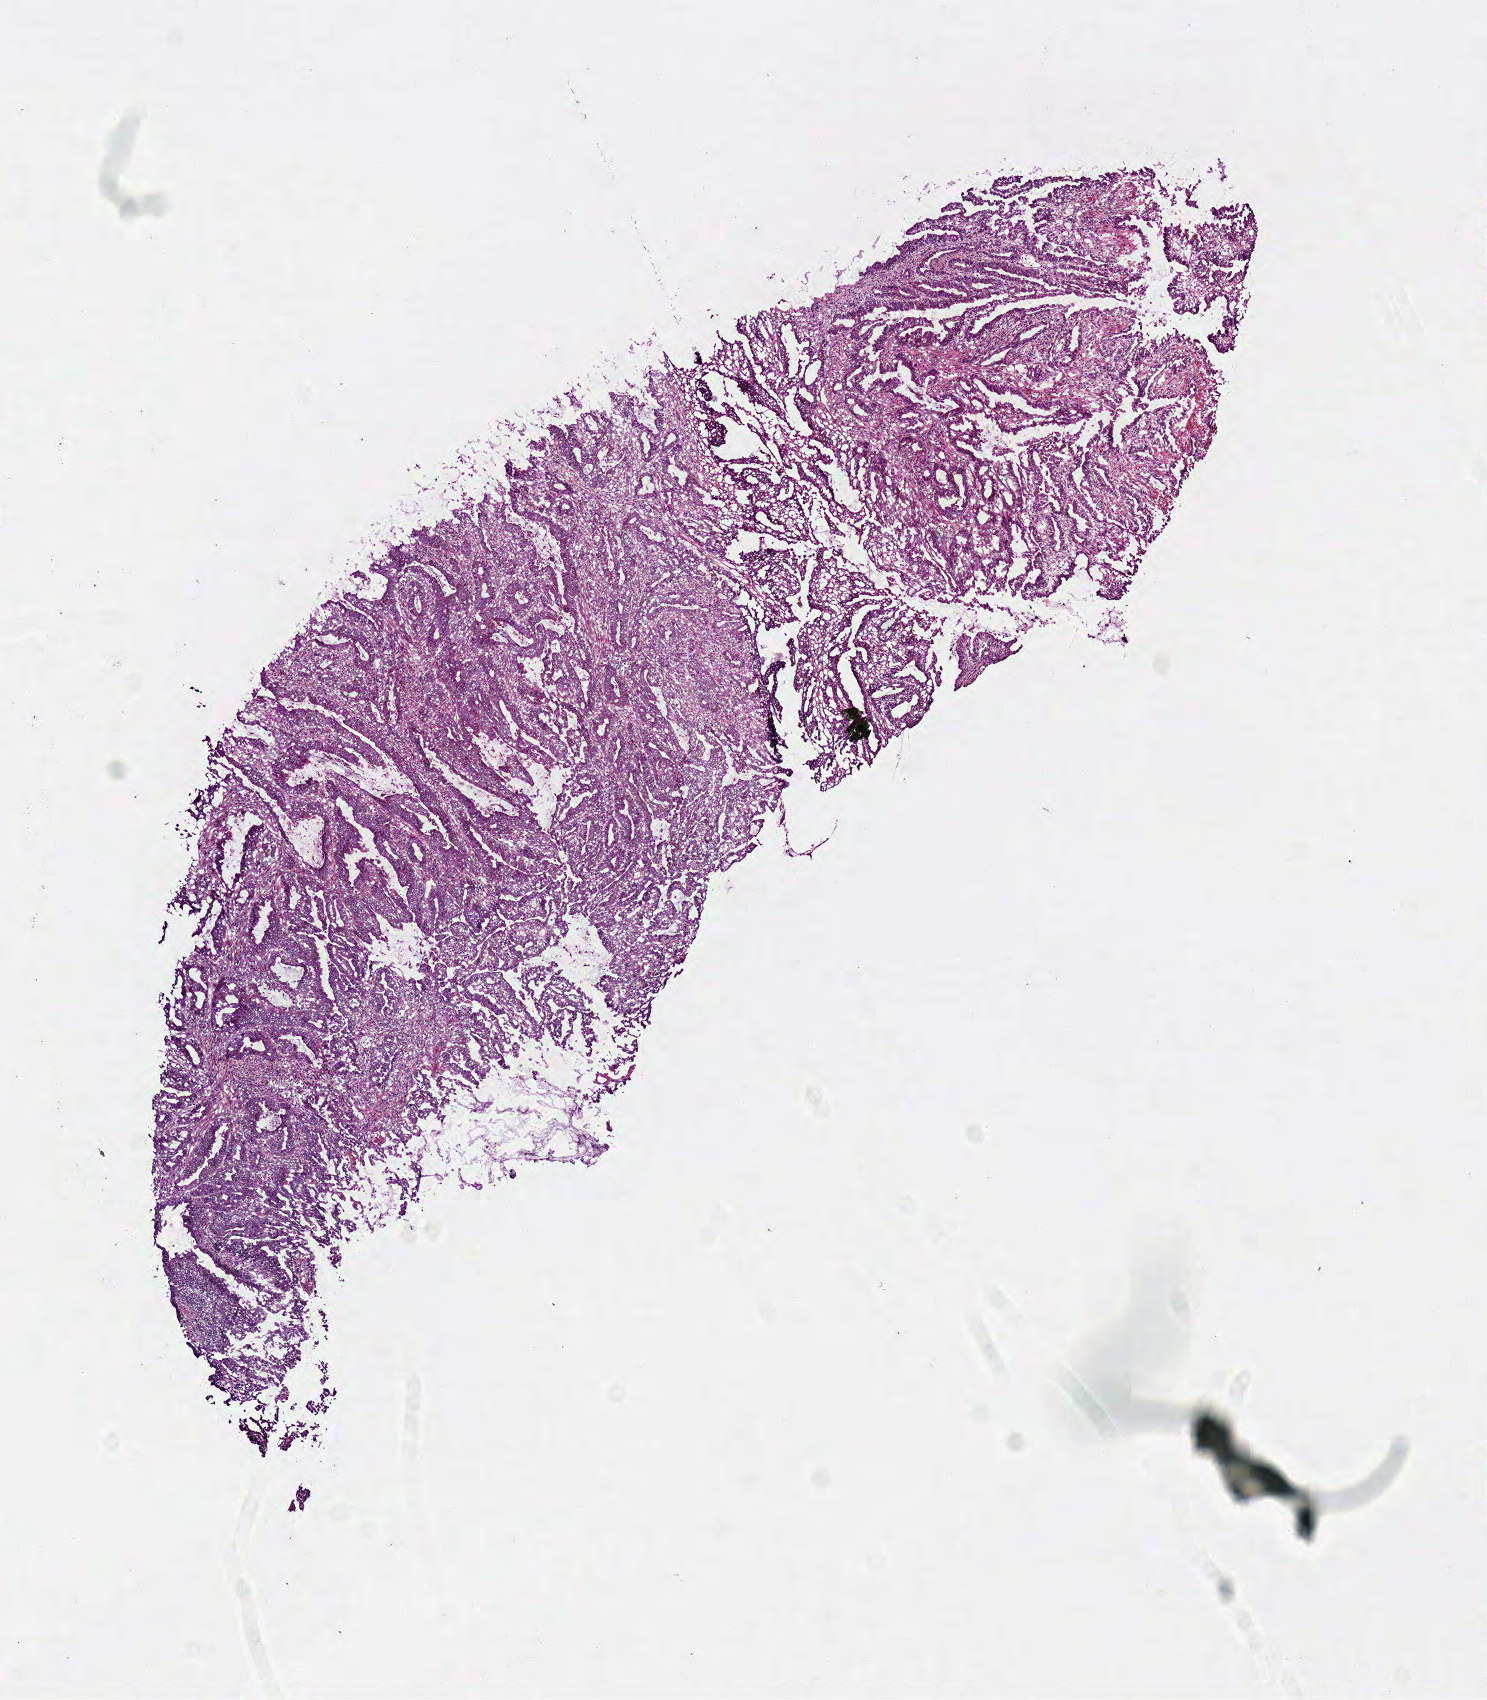
Whole-slide histology image, Hematoxylin and eosin (H&E) stained — shown as a low-resolution overview of the whole scanned area (about 5.9 x 6.7 mm, acquisition: 40x scan); frozen section from the top of the tissue portion; primary tumour sample from the colon. Male patient; age at initial diagnosis 67 years. Pathologist review of this section (percent, as recorded): tumour cells 85%, tumour nuclei 85%.
Histologic diagnosis: Mucinous adenocarcinoma.